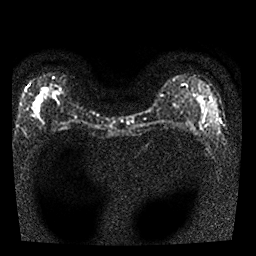
Breast MRI, one axial slice. Slice 16 of 25 in the series (ordered by position). Diffusion-weighted series; image 2 of 4 stored at this slice position (different b-values; order by instance number). 1.5 T. 256 × 256 image matrix, field of view 300 × 300 mm. Female patient.
Outlined on this slice (outlined manually by an expert reader):
- tumour on diffusion-weighted imaging: bounding box [x1, y1, x2, y2] px = [30, 96, 40, 112]